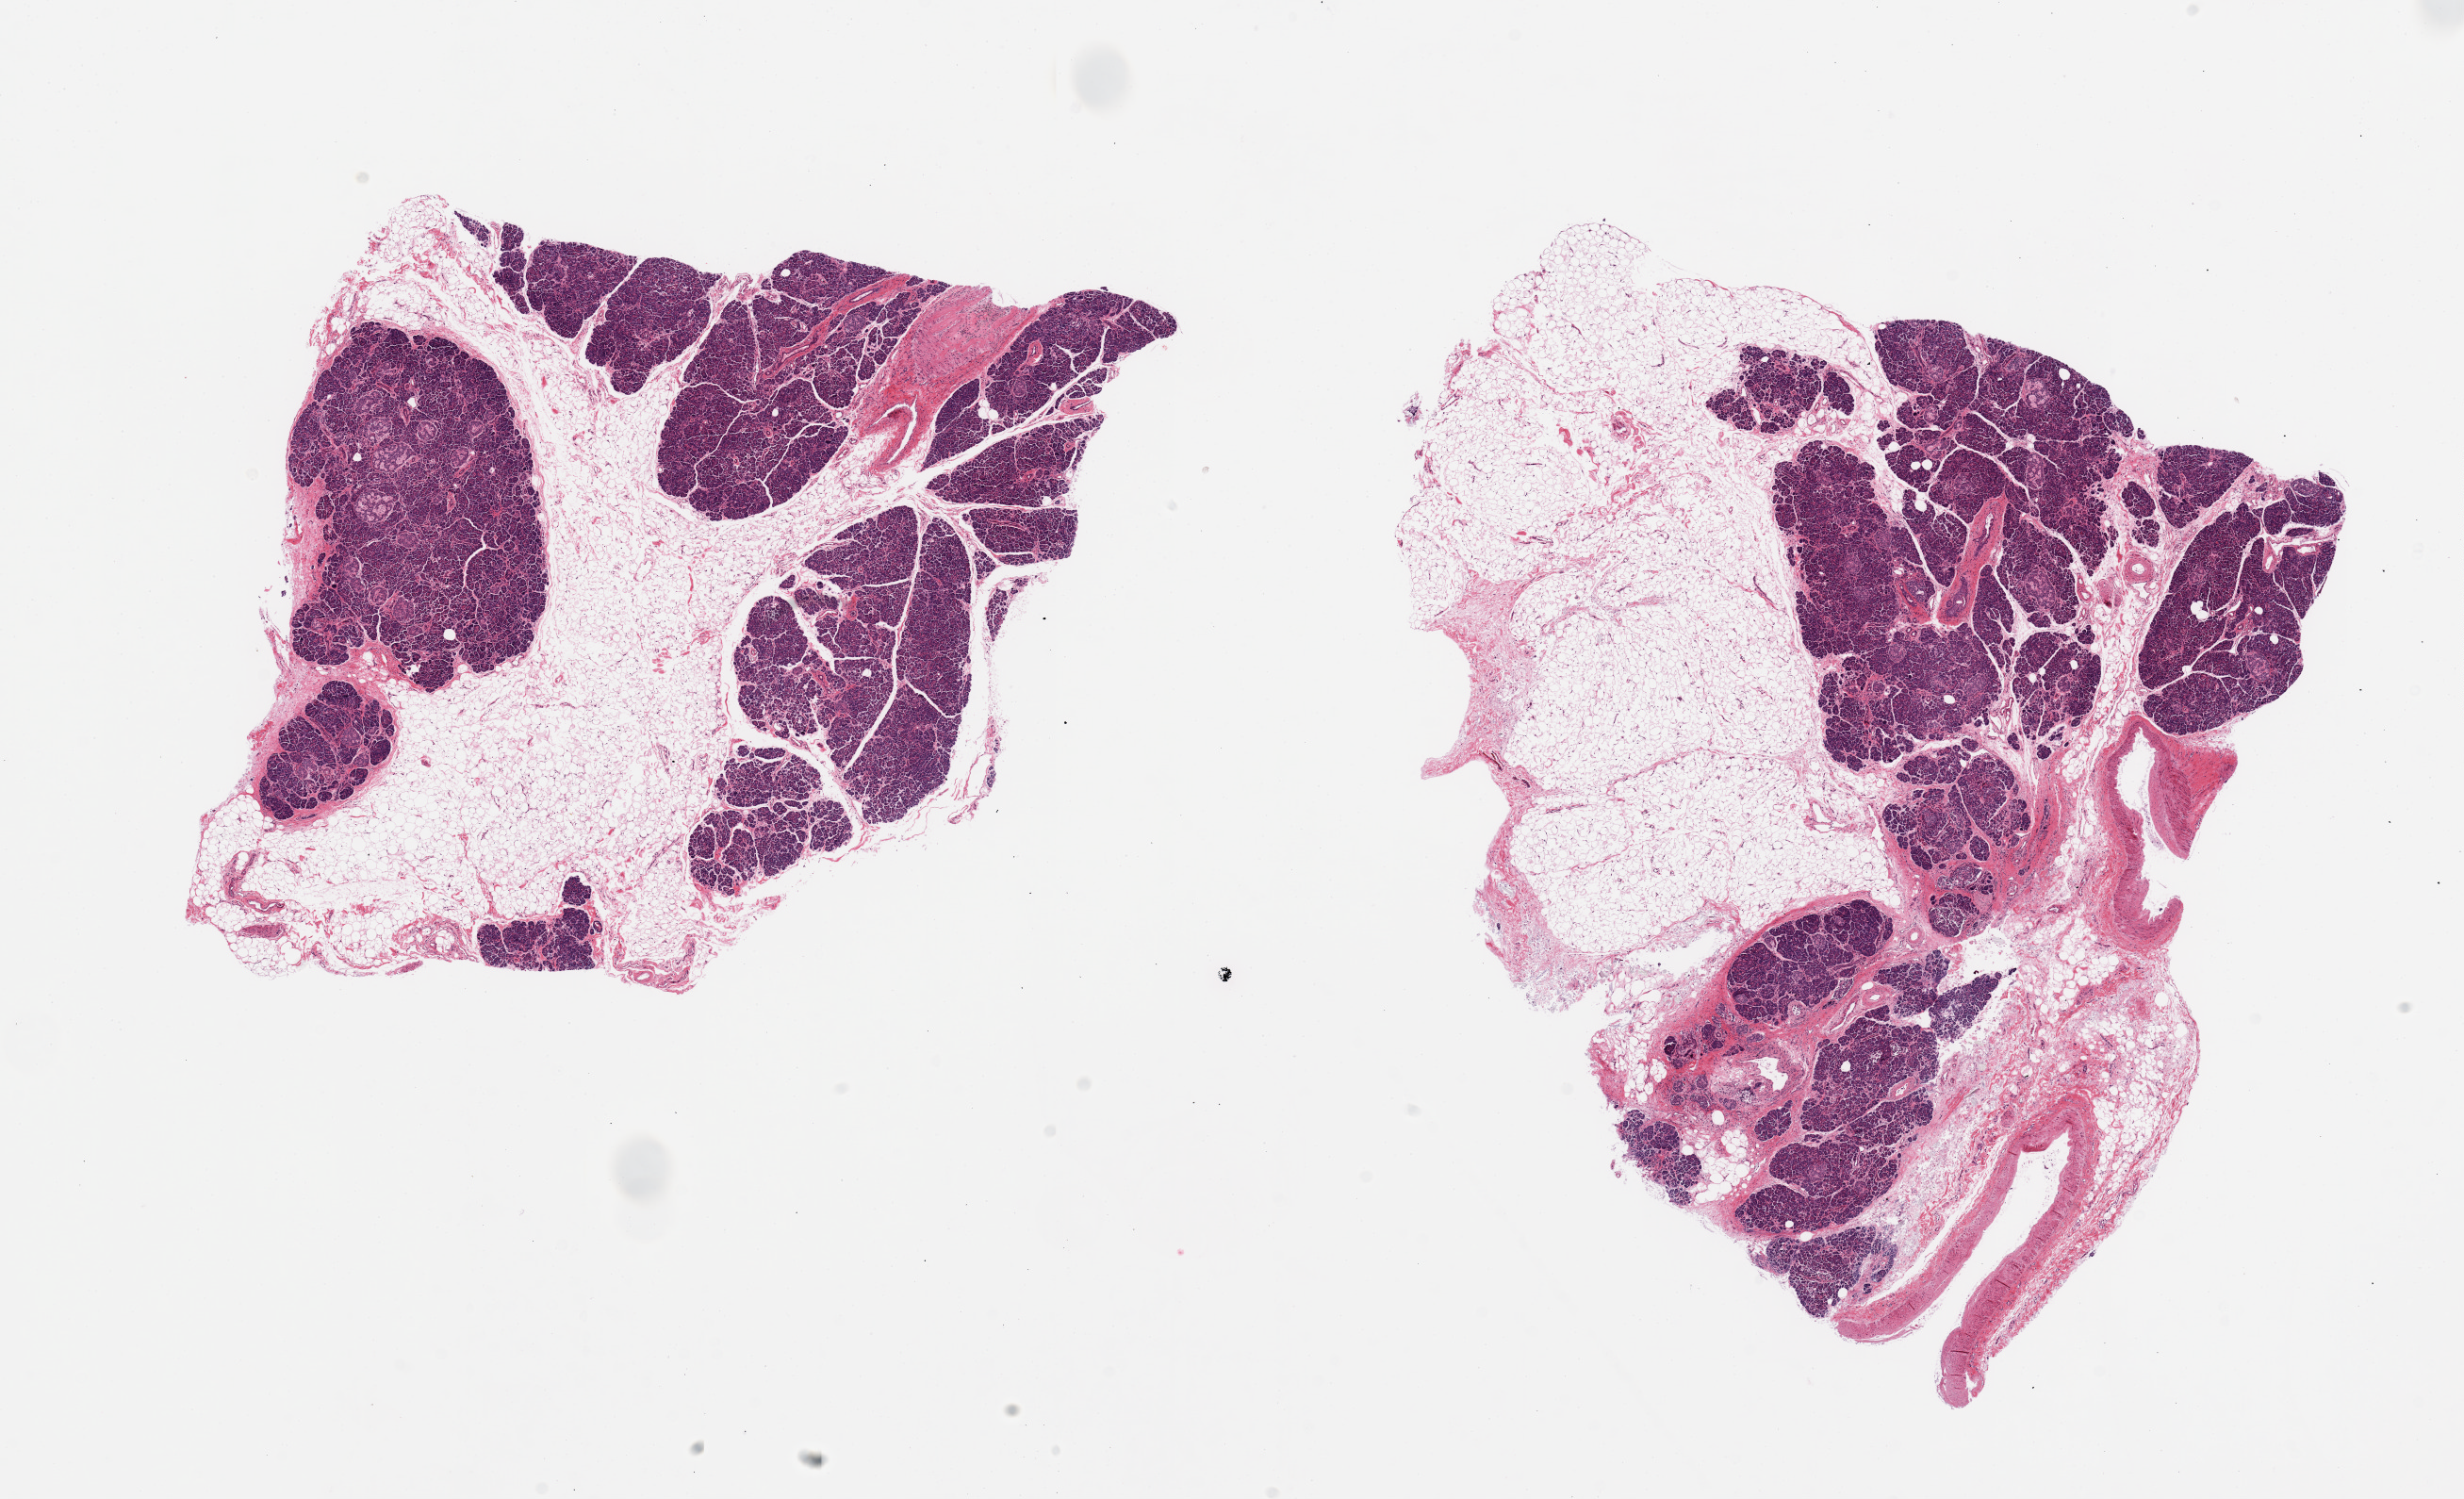
Digitized haematoxylin and eosin-stained section, brightfield, shown as a low-resolution overview of the whole scanned area (about 20.7 x 12.6 mm), PAXgene-fixed paraffin-embedded (PFPE) section, sampled site (target tissue): pancreas, tissue donor sample. Female donor.
Review note (as recorded): 2 pieces, only 40 and 60% pancreatic parenchyma with abundant fat and large vessels, focal islets with amyloid-like material, squamous and mucinous metaplsia in ducts.